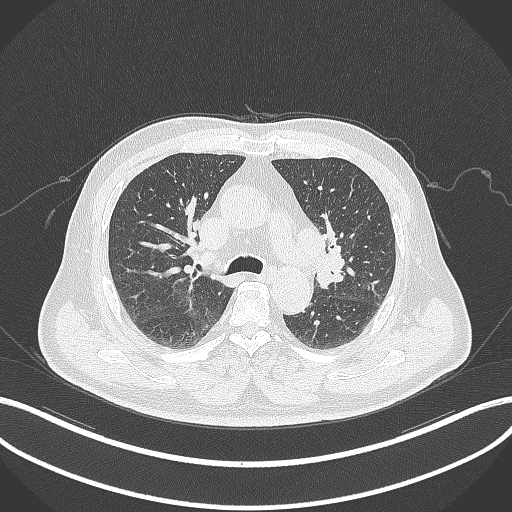
Chest CT, one axial slice. Slice 193 of 286 in the series (ordered by position). Lung window (W 1500 / L -600 HU). 1 mm slice thickness. 512 × 512 image matrix, field of view 400 × 400 mm. Patient: male, 67 years. From the clinical record (not read from this slice): clinical TNM (as recorded): T2a N1 M0; histopathological grade: G3.
Outlined on this slice (bounding box drawn by a radiologist):
- lung tumour (recorded histology: adenocarcinoma): bounding box <322,220,344,282> (left, top, right, bottom; pixels)